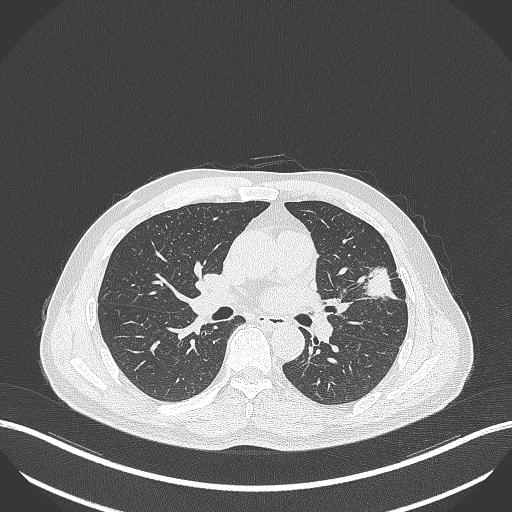
Chest CT, one axial slice. Position 218 of 418 along the scan axis. Reconstruction kernel B70f. Lung window (W 1500 / L -600 HU). 512 × 512 image matrix. Male patient, age 55 years. From the clinical record (not read from this slice): clinical TNM (as recorded): T1c N0 M0; histopathological grade: G2-3.
Outlined on this slice (rectangle marked by the reading radiologist):
- lung tumour (recorded histology: adenocarcinoma): bounding box <363,261,404,302> (left, top, right, bottom; pixels)